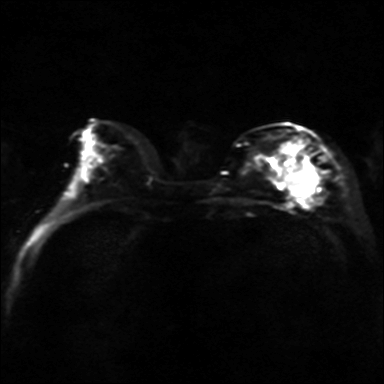
Breast MRI, one axial slice. Position 16 of 36 along the scan axis. Diffusion-weighted series; image 2 of 4 stored at this slice position (different b-values; order by instance number). 3 T. 384 × 384 image matrix, field of view 320 × 320 mm. Female patient.
Annotated regions visible in this slice (expert manual segmentation):
- tumour on diffusion-weighted imaging: bounding box (x1, y1, x2, y2) in pixels: (287, 169, 316, 198)